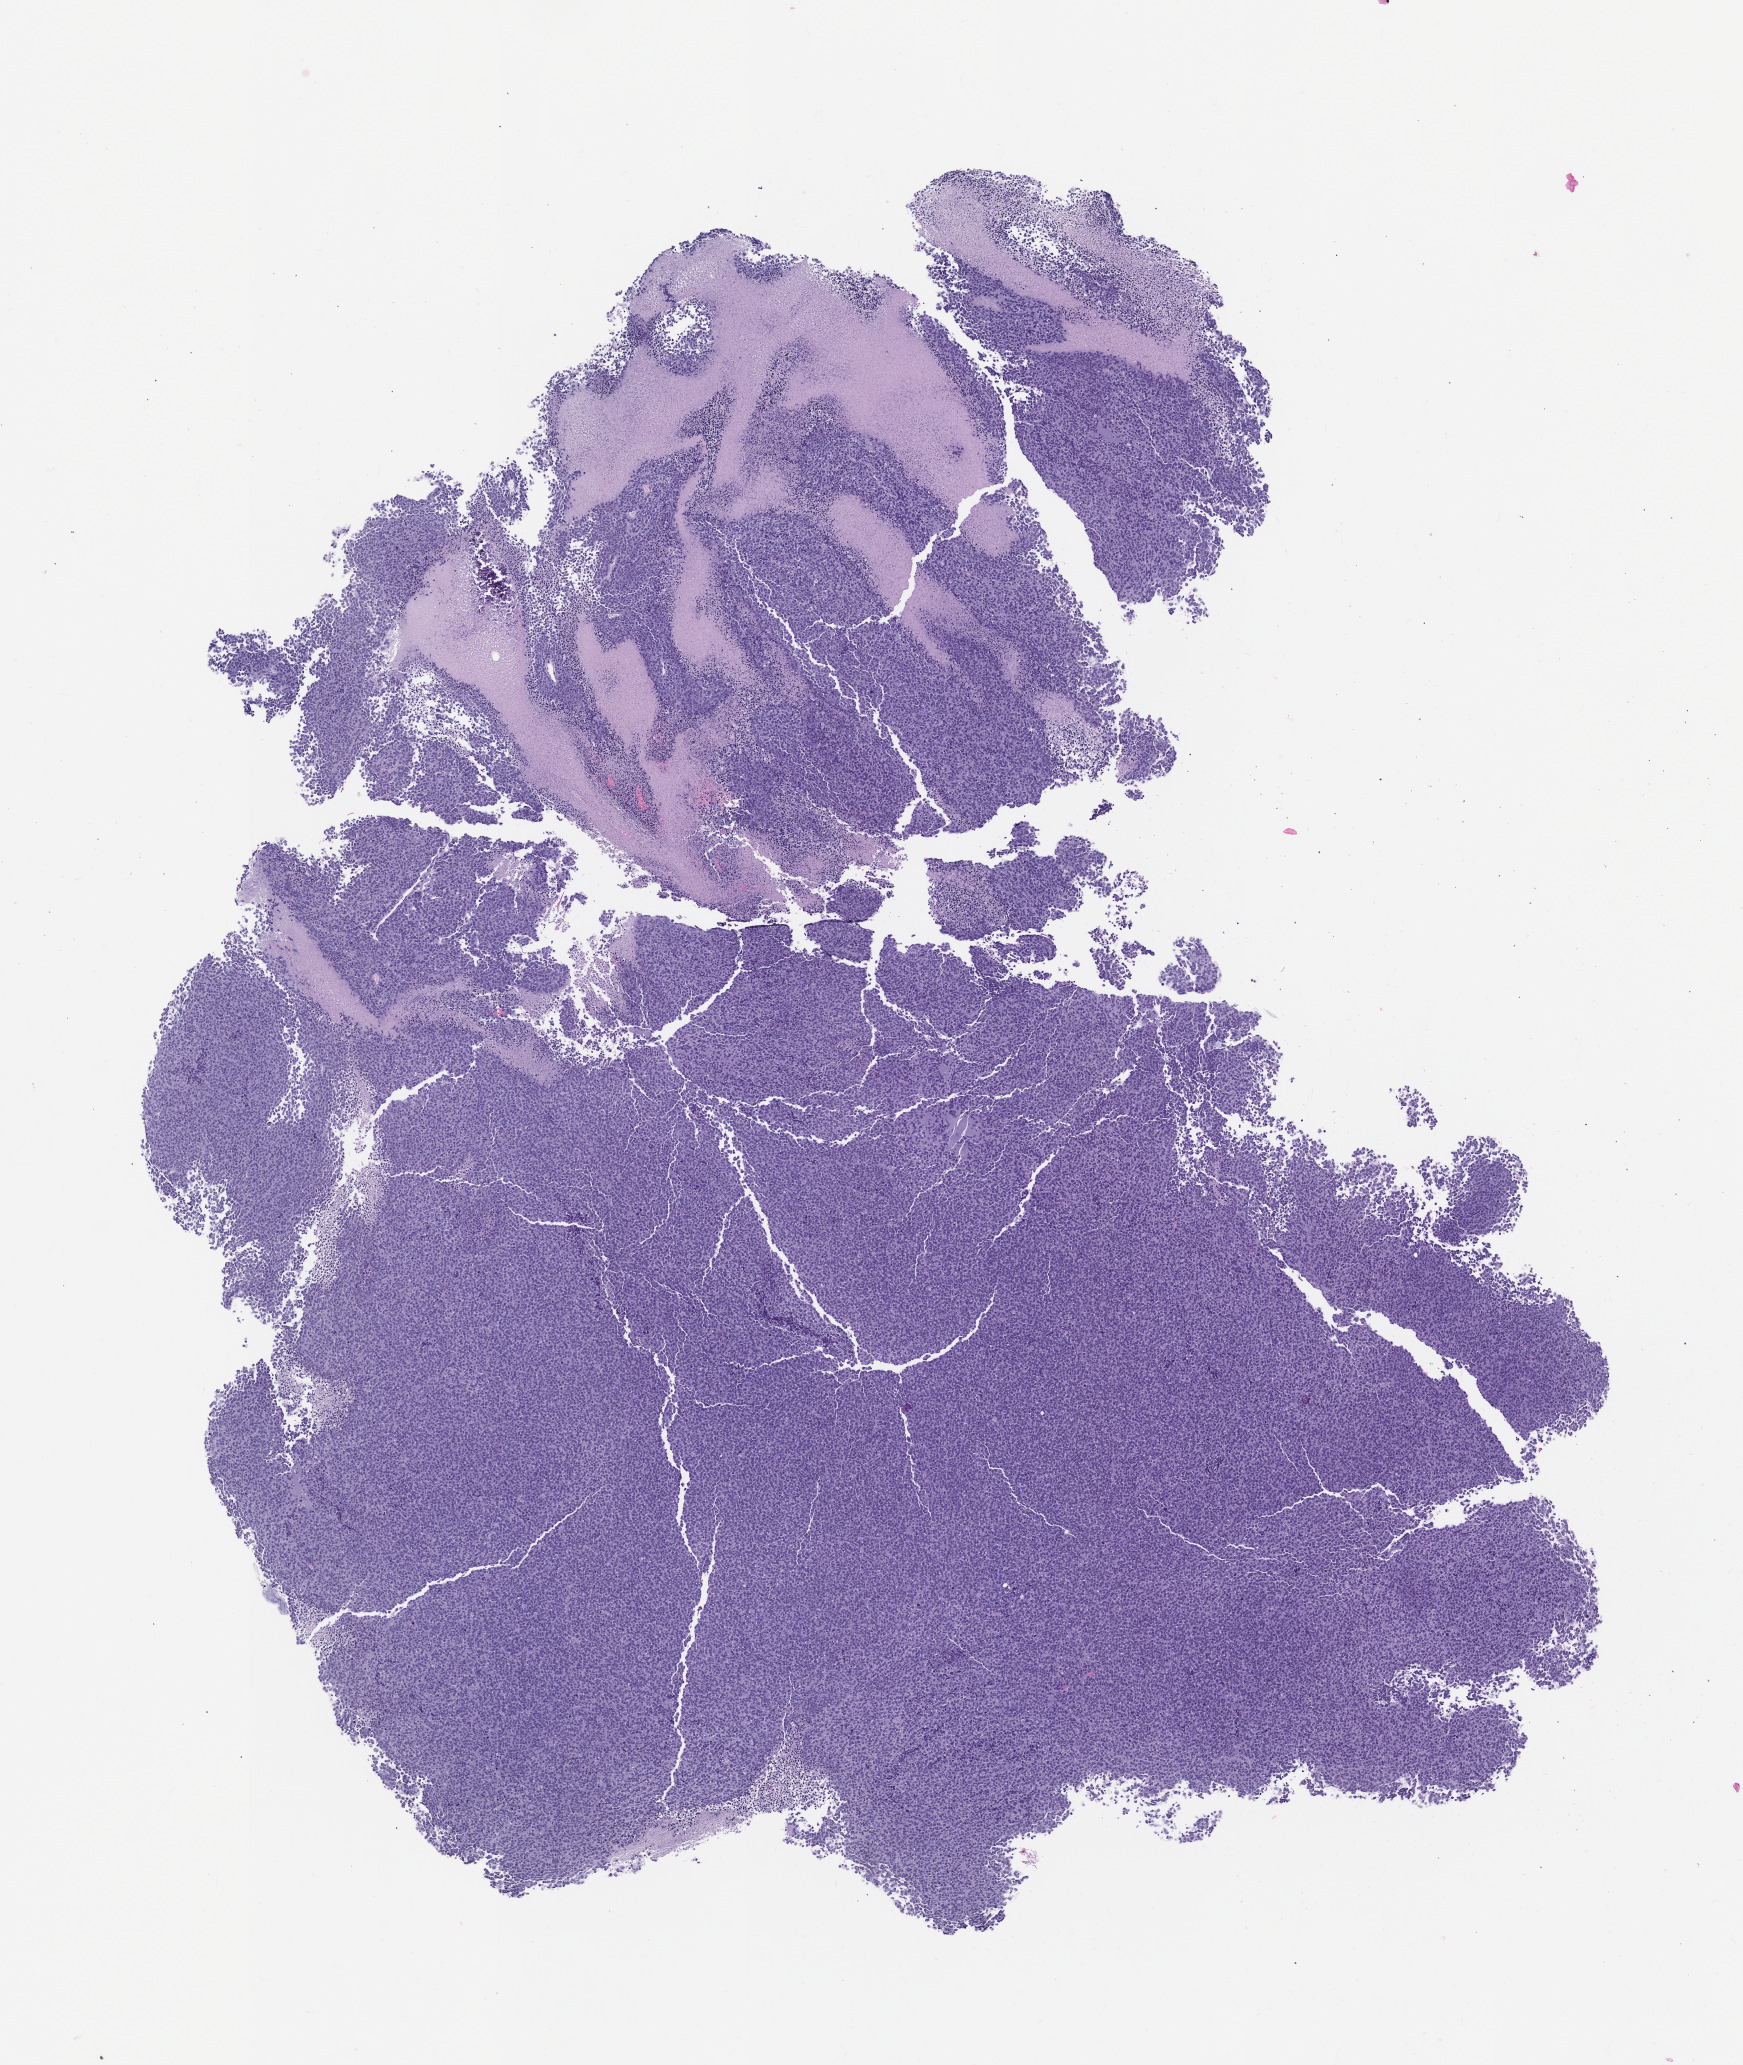
Hematoxylin and eosin (H&E) whole-slide image of a patient-derived xenograft (PDX) tumor grown in a mouse, passage 1, shown as a low-resolution overview of the whole scanned area (about 7.0 x 8.3 mm), FFPE section, originating tumor site category: musculoskeletal.
Originating patient diagnosis: Ewing Sarcoma|Primitive Neuroectodermal Tumor.